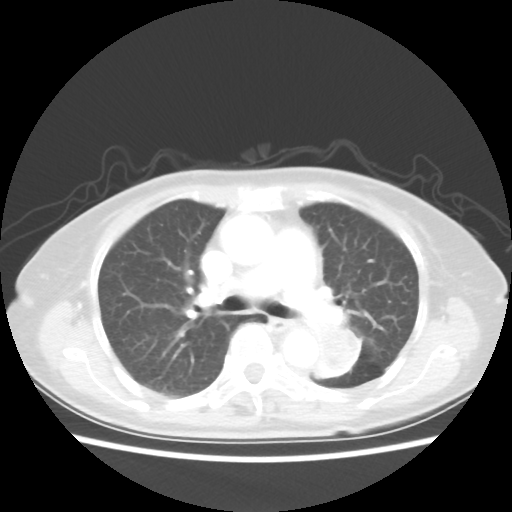
Chest CT, one axial slice; position 31 of 50 along the scan axis; lung window (W 1500 / L -600 HU); 5 mm slice thickness; 512 × 512 image matrix, field of view 335 × 335 mm. Patient: female, 81 years. From the clinical record (not read from this slice): clinical TNM (as recorded): T2 N0 M1a.
Outlined on this slice (bounding box drawn by a radiologist):
- lung tumour (recorded histology: squamous cell carcinoma): bounding box (x1, y1, x2, y2) in pixels: (308, 317, 366, 386)